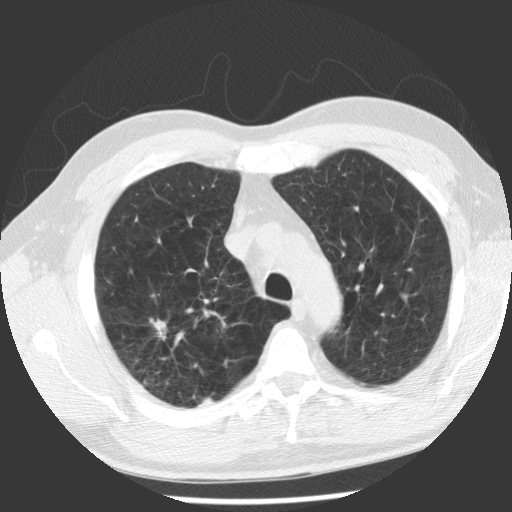
Axial slice from a low-dose chest CT screening exam. First (baseline) screen. Lung window (W 1500 / L -600 HU). 2.5 mm slice thickness. 140 kVp. 512 × 512 image matrix. Male, age 62 years at enrolment. Former smoker at enrolment.
Lesion marked by an expert reader, bounding box (x1, y1, x2, y2) in pixels: (117, 301, 195, 380). The screening reader recorded 2 non-calcified nodules or masses ≥4 mm on this exam (right upper lobe, right upper lobe); which of them this box marks is not recorded. Official screen result: positive, change unspecified: nodule(s) >= 4 mm or enlarging nodule(s), mass(es), or other non-specific abnormalities suspicious for lung cancer. Later outcome: lung cancer diagnosed 71 days after this screen — adenocarcinoma, NOS, right upper lobe, poorly differentiated (G3), stage IV (AJCC 6th edition), 30 mm at pathology.